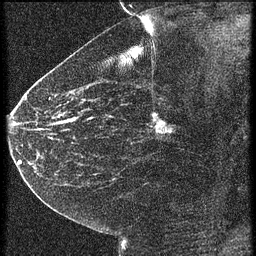
Breast MRI (dynamic contrast-enhanced), one sagittal slice. Position 34 of 60 along the scan axis. 4 images stored at this slice position (order not interpretable as contrast timing). 1.5 T. TE 4.2 ms, TR 21.3 ms. 1.5 mm slice thickness. 256 × 256 image matrix, field of view 180 × 180 mm. Female patient, age 43 years. From the clinical record (not read from this slice): setting: breast cancer imaged before/during neoadjuvant chemotherapy; receptor status: HER2-positive.
Annotated regions visible in this slice (semi-automatically segmented with operator editing):
- analysis volume of interest (the breast-tissue region the enhancement analysis was run in; not a lesion): box from (x=122, y=100) to (x=187, y=151) px
- tumour enhancement mask (voxels above the 90 % enhancement threshold inside the analysis volume of interest): (x=152, y=114)–(x=171, y=133)